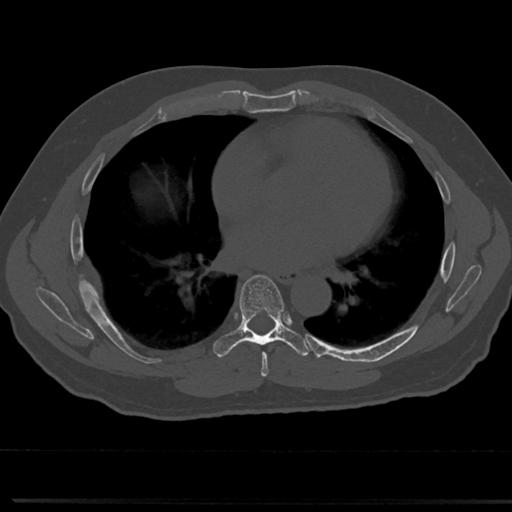
CT including the spine, one axial slice. Slice 413 of 817 in the series (ordered by position). Bone window (W 1800 / L 400 HU). 0.5 mm slice thickness. 512 × 512 image matrix. Patient: male, 61 years. From the clinical record (not read from this slice): primary cancer: prostate.
Structures marked on this image (semi-automatic segmentation, software-assisted and operator-edited):
- T6 vertebra: box from (x=246, y=333) to (x=319, y=365) px
- T7 vertebra: (x=218, y=274)–(x=286, y=355)